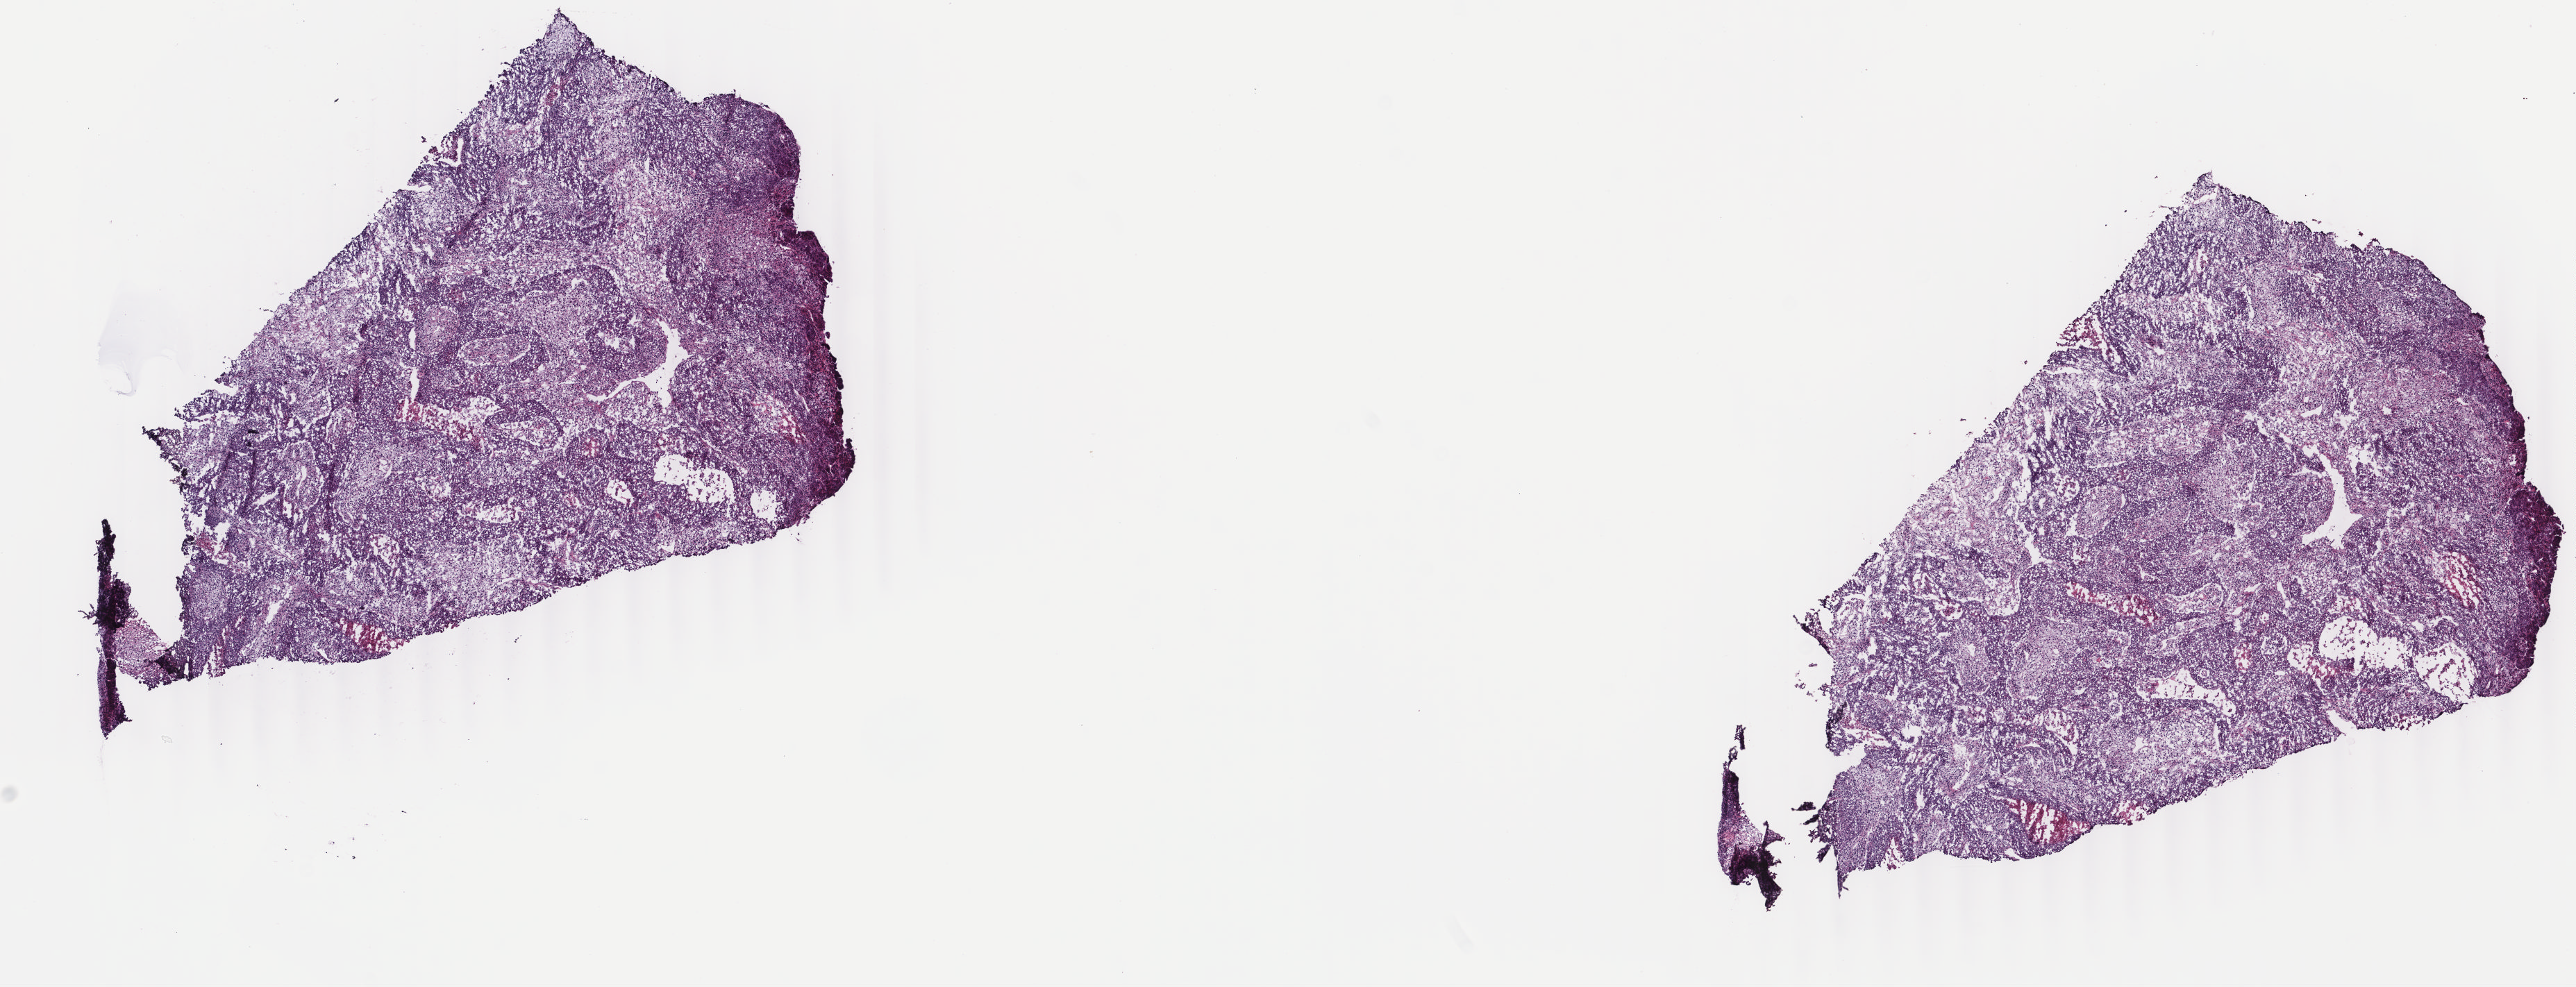
Digitized H&E-stained tissue section (whole slide) — whole scanned area (about 14.8 x 5.7 mm) shown as a low-resolution overview. Frozen section from the top of the tissue portion. Sample: primary tumour, uterus. Female, age 70 years at initial diagnosis. Histologic grade: G3 (poorly differentiated). Slide review estimates, as recorded: tumour cells 80%, tumour nuclei 80%, normal cells 0%, stromal cells 10%, necrosis 10%. Infiltration values recorded for this section: lymphocyte infiltration 30%, monocyte infiltration 30%, neutrophil infiltration 30%.
Lymph nodes positive (case pathology): 3 of 3 examined. Histologic diagnosis: Endometrioid adenocarcinoma, NOS (endometrium). FIGO stage: IIIC.